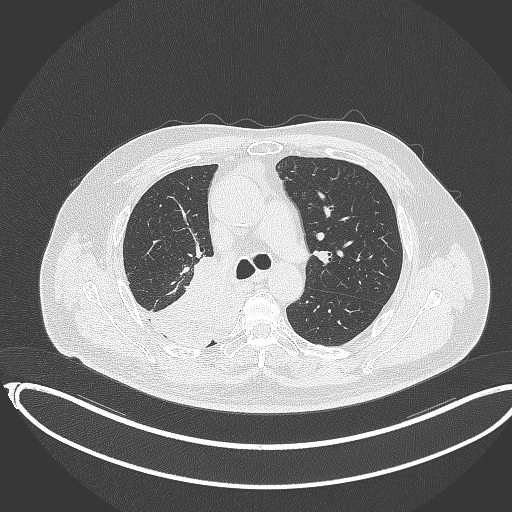
Chest CT, one axial slice. Position 237 of 403 along the scan axis. Reconstruction kernel B70f. 120 kVp. Lung window (W 1500 / L -600 HU). 1 mm slice thickness. 512 × 512 image matrix, field of view 436 × 436 mm. Male patient, age 68 years. From the clinical record (not read from this slice): clinical TNM (as recorded): T2a N0 M0.
Outlined on this slice (rectangle marked by the reading radiologist):
- lung tumour (recorded histology: adenocarcinoma): box from (x=125, y=260) to (x=235, y=349) px